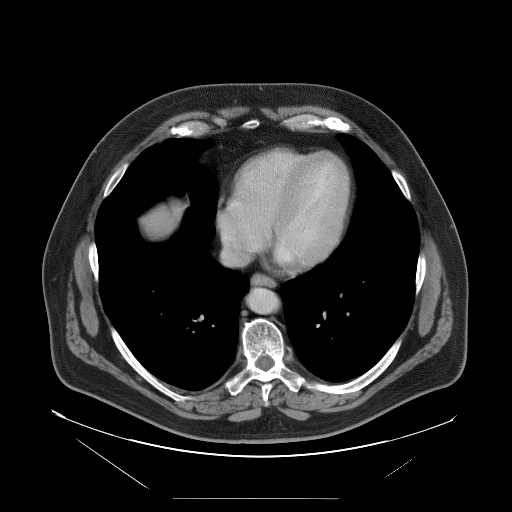
Contrast-enhanced abdominal CT, one axial slice. Position 100 of 114 along the scan axis. 120 kVp. Intravenous contrast given. Soft-tissue window (W 400 / L 40 HU). 5 mm slice thickness. 512 × 512 image matrix. Male patient, age 61 years. From the clinical record (not read from this slice): diagnosis: colorectal cancer liver metastases, imaged before liver resection; multiple liver metastases: no; largest metastasis: 6.5 cm.
Annotated regions visible in this slice (manually delineated by an expert):
- hepatic veins: bounding box <220,214,268,265> (left, top, right, bottom; pixels)
- liver: <141,208,177,242>